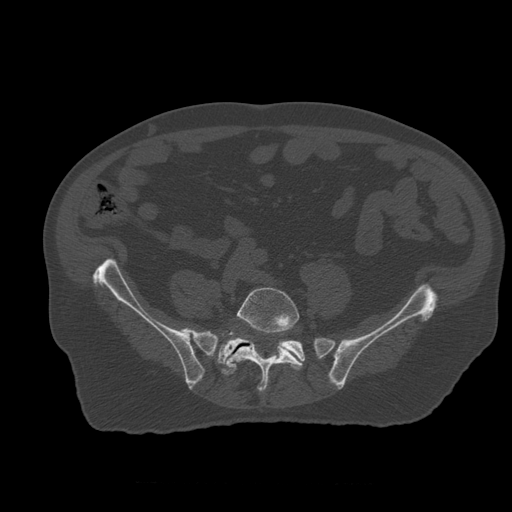
CT including the spine, one axial slice; position 136 of 399 along the scan axis; bone window (W 1800 / L 400 HU); 1.25 mm slice thickness; 512 × 512 image matrix. Patient age 73 years. Case-level facts recorded for this patient, not image findings: primary cancer: prostate; vertebrae with lytic lesions (as recorded): L2.
Outlined on this slice (semi-automatically segmented with operator editing):
- L5 vertebra: bounding box [x1, y1, x2, y2] px = [222, 288, 303, 392]